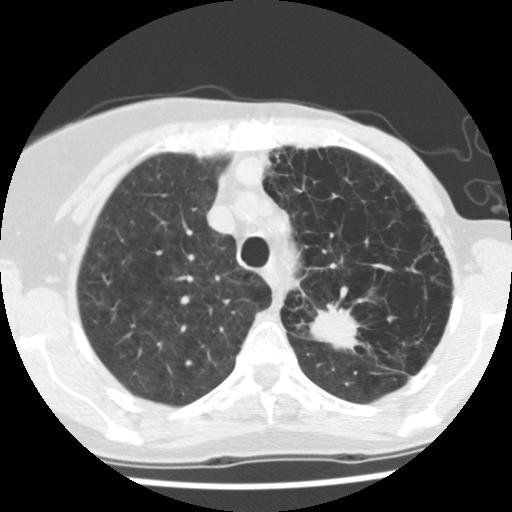
Low-dose screening chest CT, one axial slice. Slice 99 of 128 in the series (ordered by position). 140 kVp. Lung window (W 1500 / L -600 HU). 2.5 mm slice thickness. 512 × 512 image matrix.
Outlined on this slice (manually delineated by an expert):
- lesion 1 (tumor, upper lobe of left lung): box from (x=309, y=304) to (x=360, y=350) px